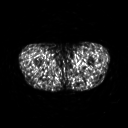
FDG PET of an extremity soft-tissue mass (from a PET/CT study), one axial slice. Position 260 of 311 along the scan axis. 3.27 mm slice thickness. 128 × 128 image matrix, field of view 500 × 500 mm. Male patient, age 29 years. Case-level facts recorded for this patient, not image findings: histological type: mixoid liposarcoma; grade: low; site of the primary tumour: left thigh.
Structures marked on this image (expert contour drawn on MRI and transferred to this co-registered scan by the dataset authors):
- gross tumour volume (mass): bounding box (x1, y1, x2, y2) in pixels: (74, 57, 81, 65)